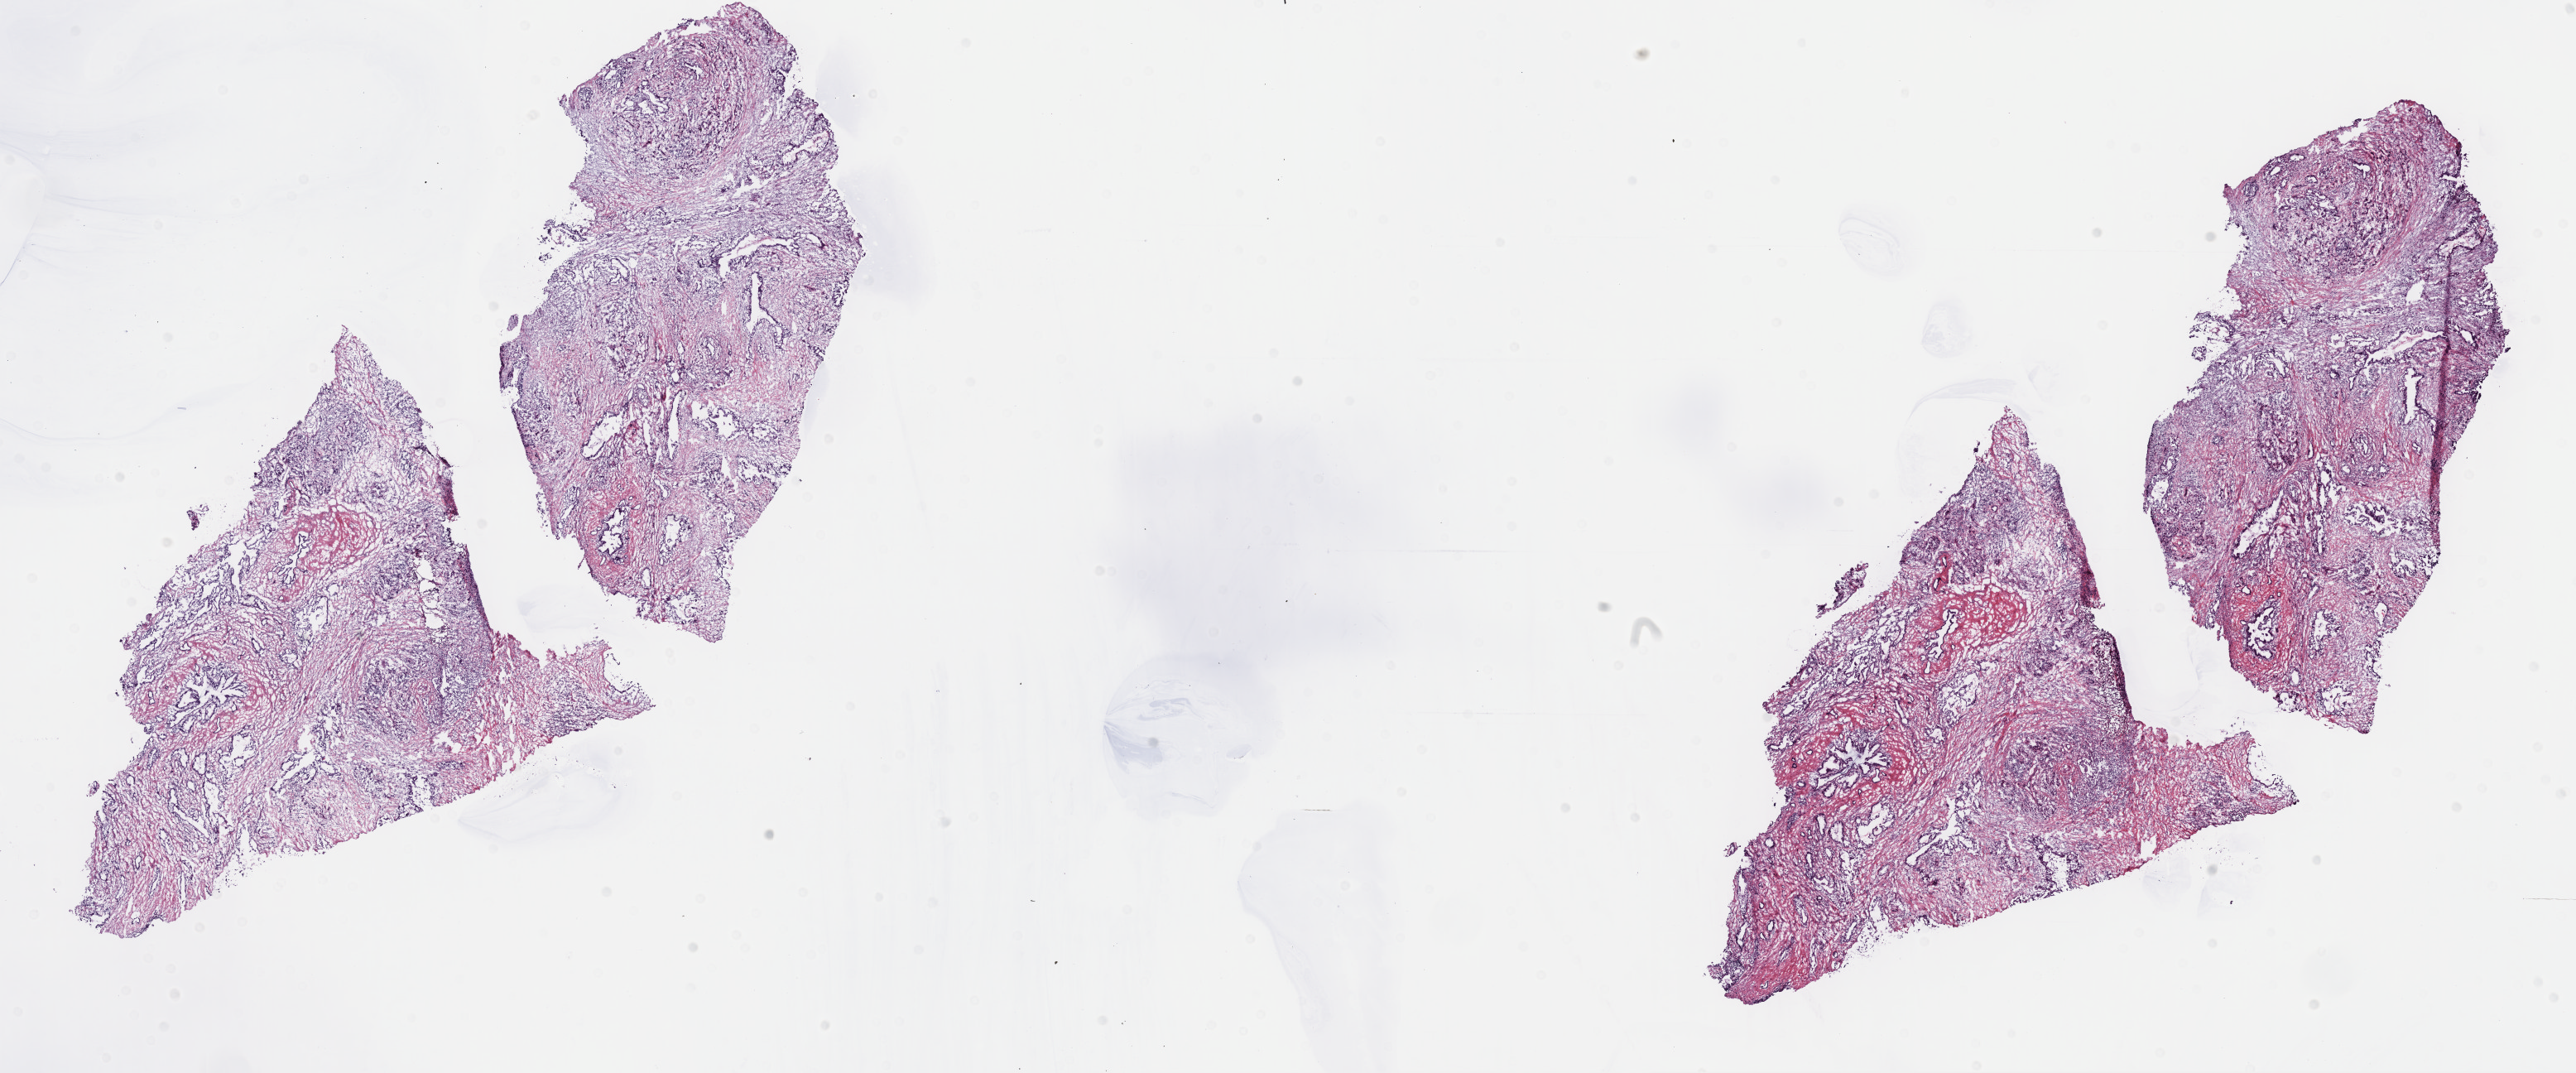
H&E whole-slide image — a low-resolution overview of the entire scanned area, about 25.2 x 10.5 mm (acquisition: 40x scan); frozen section from the top of the tissue portion; pancreas, primary tumour sample. Male patient; age at initial diagnosis 71 years. Histologic grade: G2 (moderately differentiated). Pathologist review of this section (percent, as recorded): tumour cells 20%, tumour nuclei 20%, normal cells 30%, stromal cells 50%, necrosis 0%. Inflammatory infiltration, as recorded: lymphocyte infiltration 4%, monocyte infiltration 3%, neutrophil infiltration 7%.
AJCC pathologic stage: IIB (7th edition). Diagnosis: Infiltrating duct carcinoma, NOS (head of pancreas).